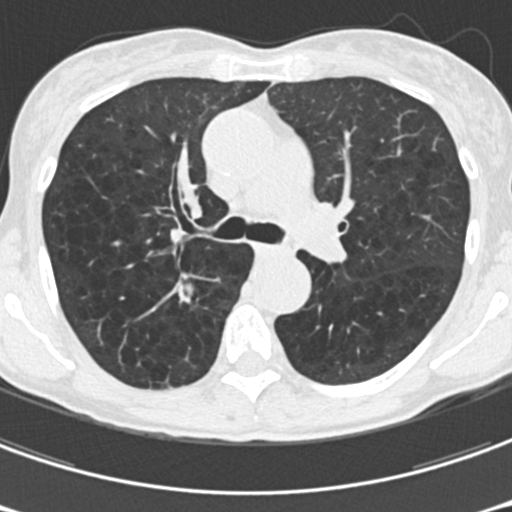
Axial slice from a low-dose chest CT screening exam. Third annual screen. Lung window (W 1500 / L -600 HU). 2 mm slice thickness. Slice 66 of 176 in the series. Female, age 61 years at enrolment. Current smoker at enrolment.
- Lesion marked by an expert reader, bounding box (x1, y1, x2, y2) in pixels: (162, 262, 226, 323).
- The screening reader recorded 2 non-calcified nodules or masses ≥4 mm on this exam (right upper lobe, right upper lobe); which of them this box marks is not recorded.
- Official screen result: positive, other.